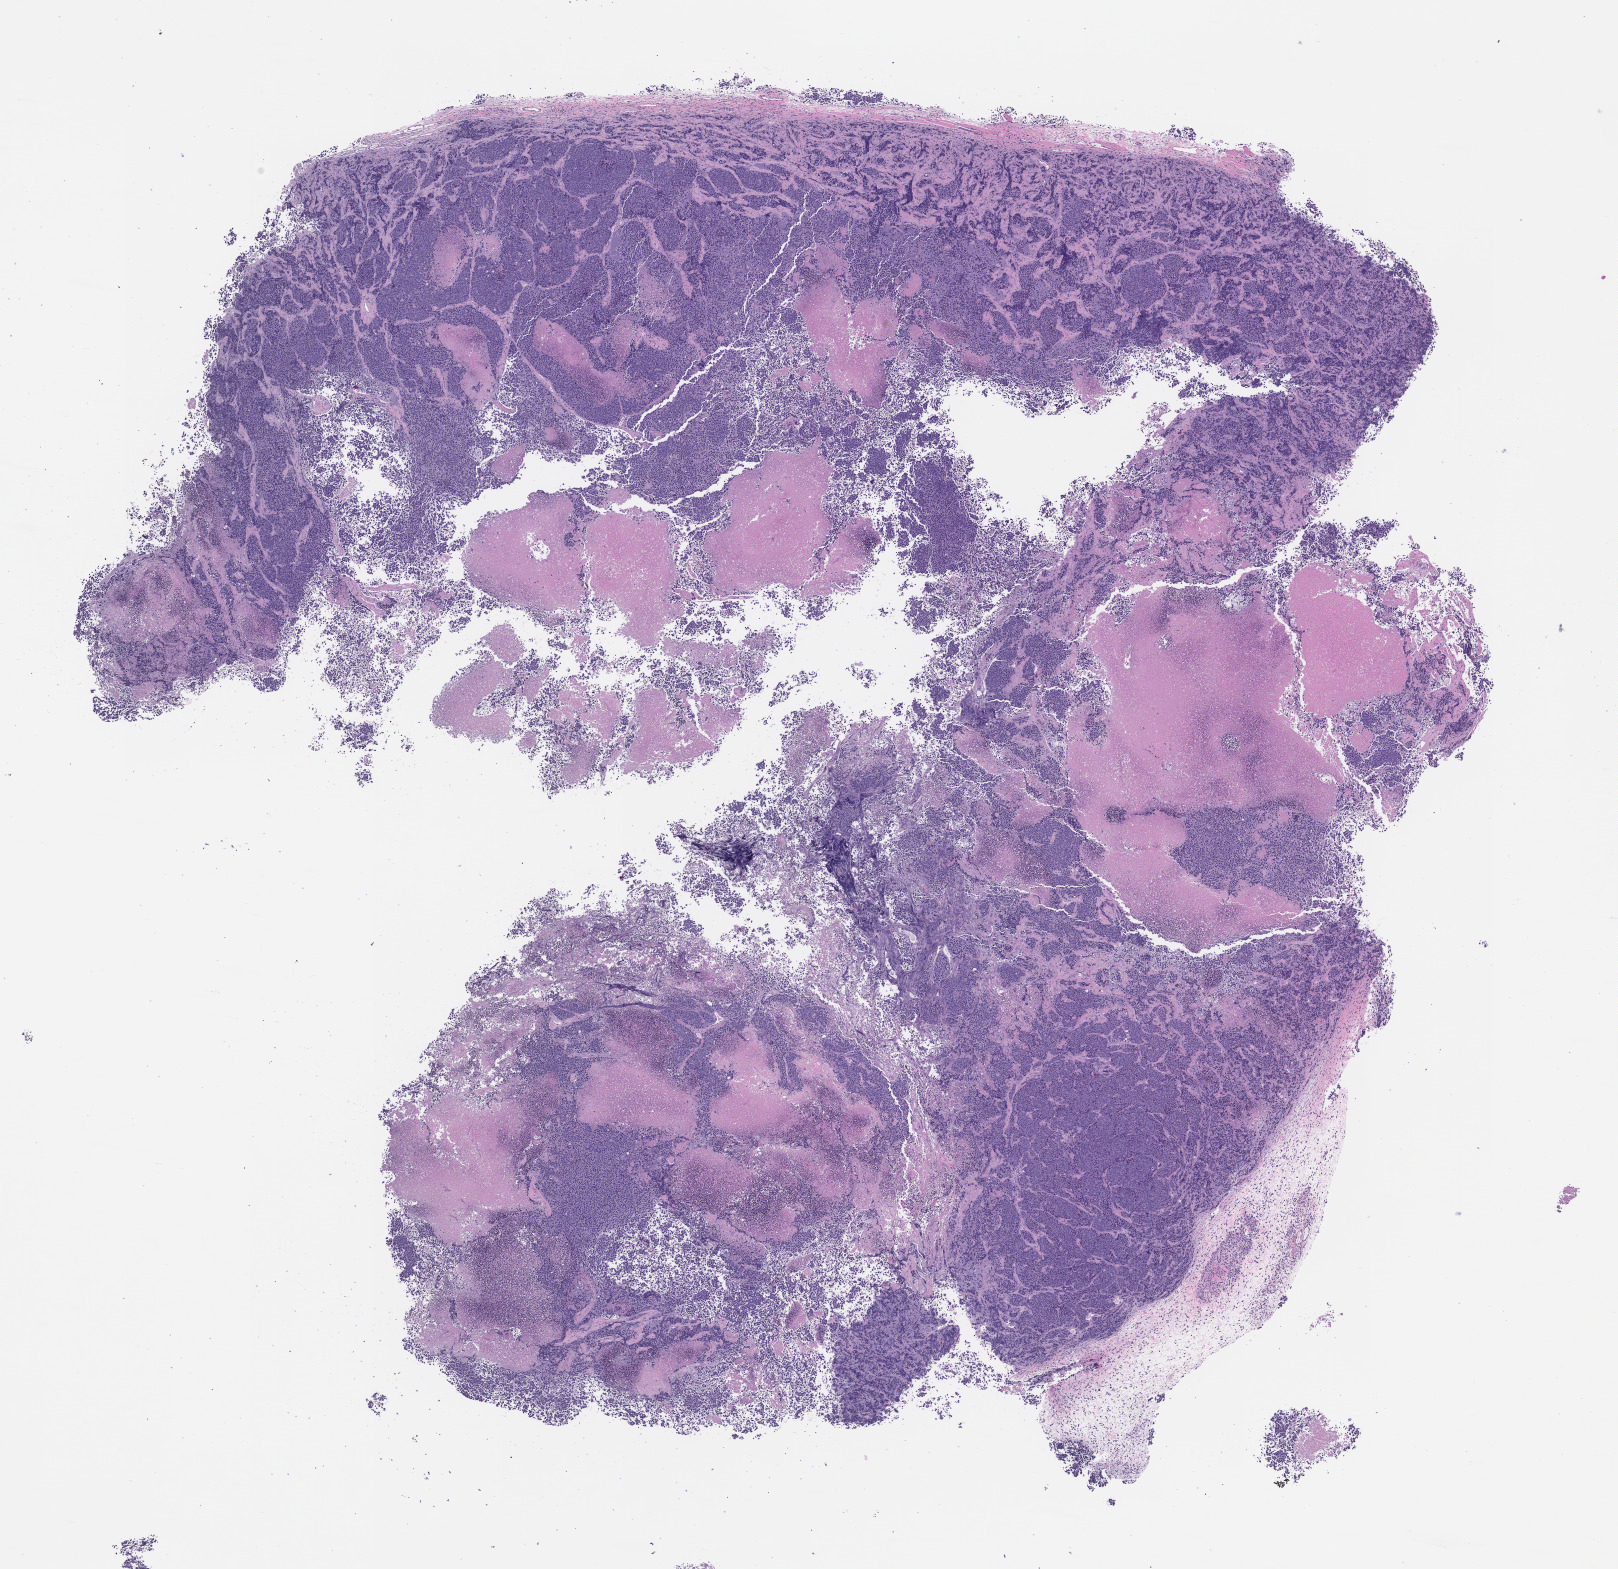
Hematoxylin and eosin (H&E) whole-slide image of a patient-derived xenograft (PDX) tumor grown in a mouse, passage 1 — shown as a low-resolution overview of the whole scanned area (about 13.0 x 12.6 mm); formalin-fixed paraffin-embedded section; originating tumor site category: neuroendocrine system.
Originating patient diagnosis: Neuroendocrine Carcinoma.